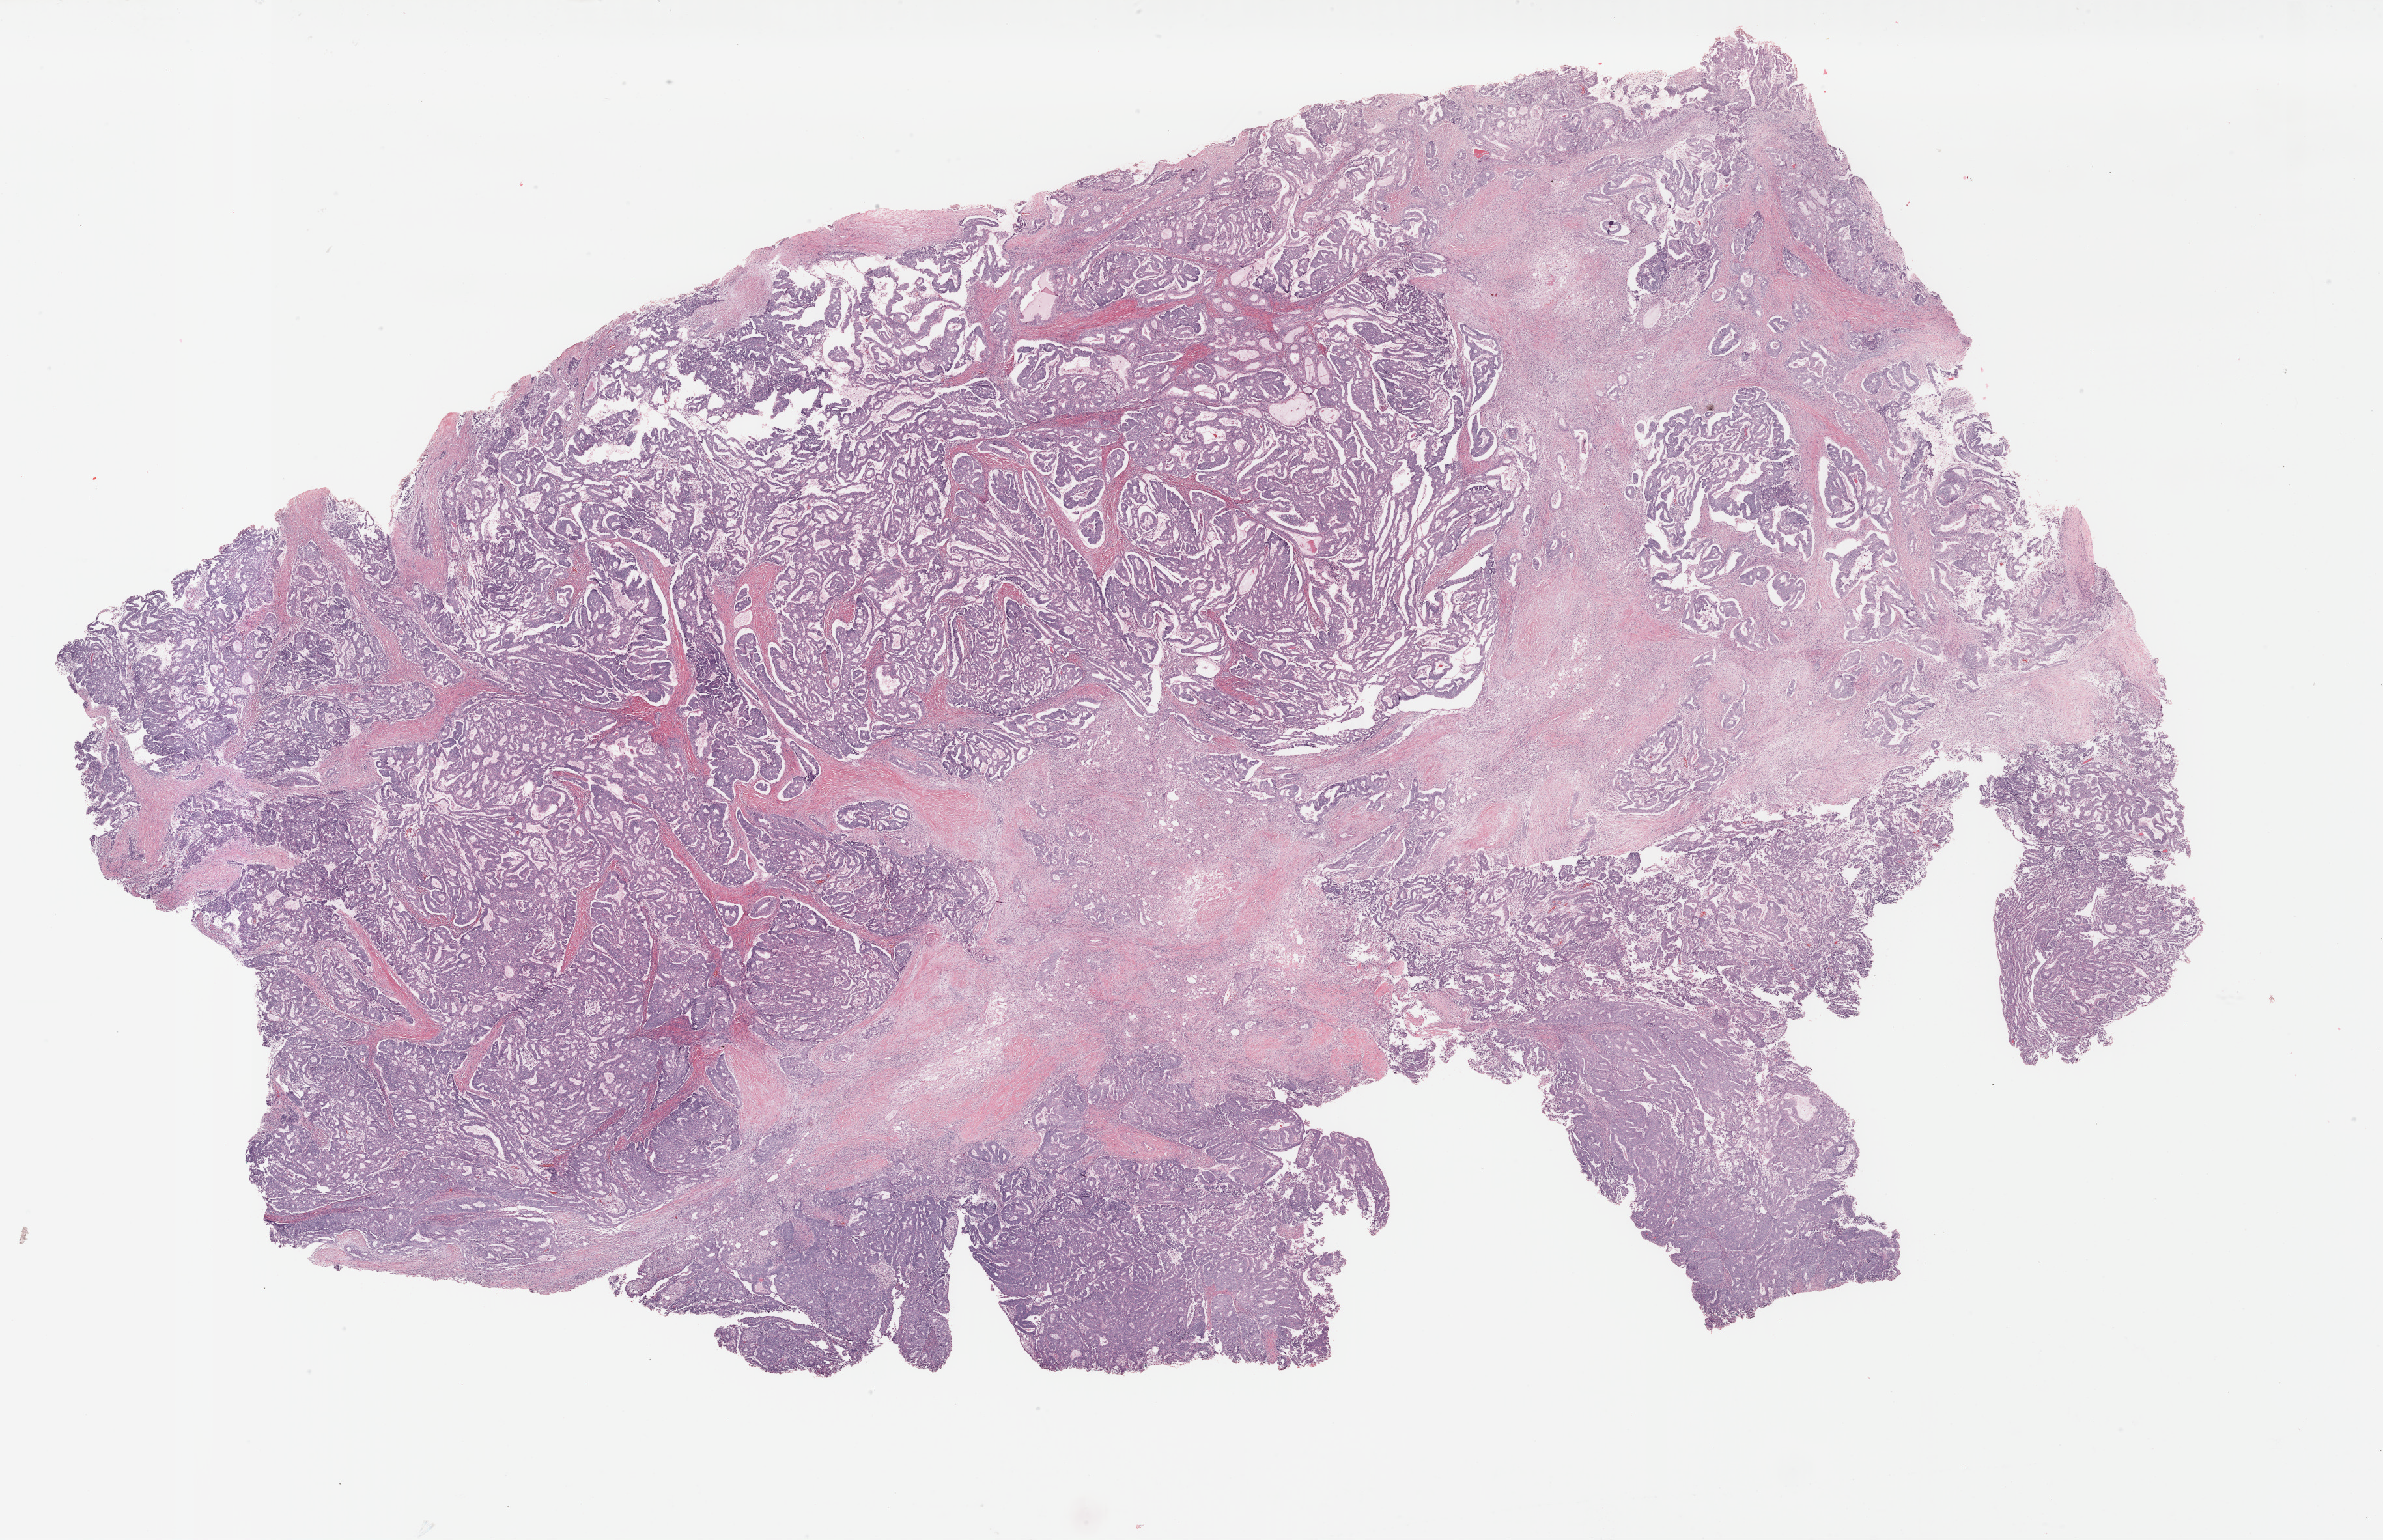
Digitized Hematoxylin and eosin (H&E) stained tissue section (whole slide) — shown as a low-resolution overview of the whole scanned area (about 29.0 x 18.8 mm). FFPE section. Uterus, primary tumour sample. Patient: female, age at initial diagnosis 59 years.
Pathologic diagnosis: Endometrioid adenocarcinoma, NOS.